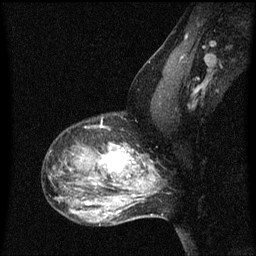
Breast MRI (dynamic contrast-enhanced), one sagittal slice. Position 42 of 60 along the scan axis. Dynamic contrast-enhanced series, image 2 of 3 at this slice position (ordered by acquisition). 1.5 T. TE 4.2 ms, TR 8 ms. 2 mm slice thickness. 256 × 256 image matrix. Female patient, age 50 years.
Outlined on this slice (semi-automatically segmented with operator editing):
- analysis volume of interest (the breast-tissue region the enhancement analysis was run in; not a lesion): bounding box [x1, y1, x2, y2] px = [91, 144, 141, 189]
- tumour enhancement mask (voxels above the 70 % enhancement threshold inside the analysis volume of interest): [103, 146, 133, 177]